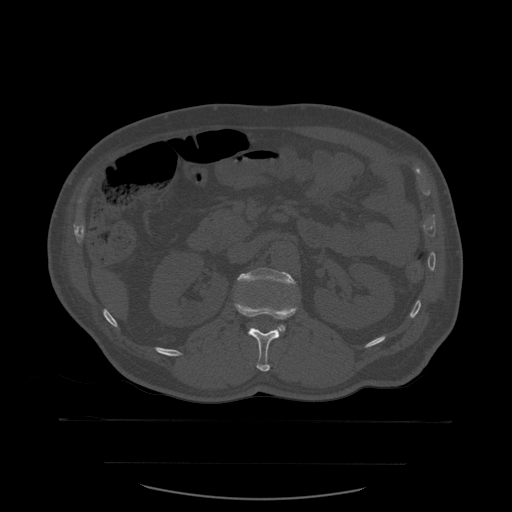
CT including the spine, one axial slice. Position 238 of 590 along the scan axis. Bone window (W 1800 / L 400 HU). 1.25 mm slice thickness. 512 × 512 image matrix, field of view 479 × 479 mm. Patient age 71 years. From the clinical record (not read from this slice): primary cancer: lung; vertebrae with lytic lesions (as recorded): T1, T2, L5, S1.
Outlined on this slice (semi-automatically segmented with operator editing):
- L1 vertebra: bounding box [x1, y1, x2, y2] px = [235, 301, 298, 372]
- L2 vertebra: [237, 268, 296, 336]